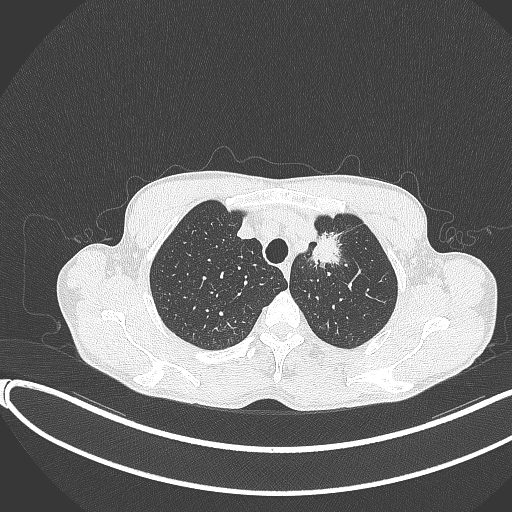
Chest CT, one axial slice; slice 319 of 374 in the series (ordered by position); 120 kVp; lung window (W 1500 / L -600 HU); 1 mm slice thickness; 512 × 512 image matrix. Male patient, age 58 years. From the clinical record (not read from this slice): clinical TNM (as recorded): T1c N1 M0.
Annotated regions visible in this slice (rectangle marked by the reading radiologist):
- lung tumour (recorded histology: adenocarcinoma): box from (x=305, y=227) to (x=354, y=276) px